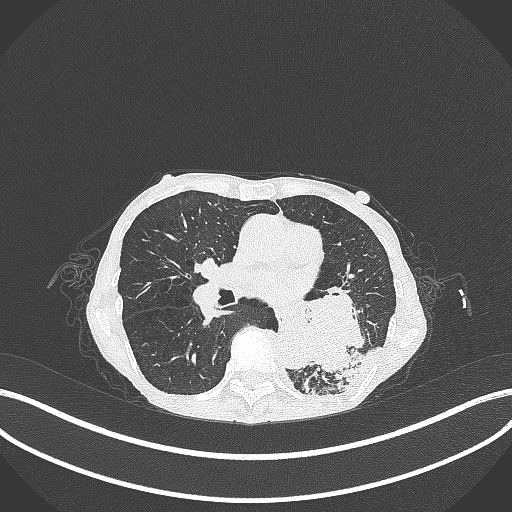
Chest CT, one axial slice; lung window (W 1500 / L -600 HU); 1 mm slice thickness; 512 × 512 image matrix, field of view 400 × 400 mm. Female patient, age 70 years. Case-level facts recorded for this patient, not image findings: clinical TNM (as recorded): T3 N0 M0; histopathological grade: G3.
Structures marked on this image (bounding box drawn by a radiologist):
- lung tumour (recorded histology: small cell carcinoma): bounding box <295,286,370,382> (left, top, right, bottom; pixels)